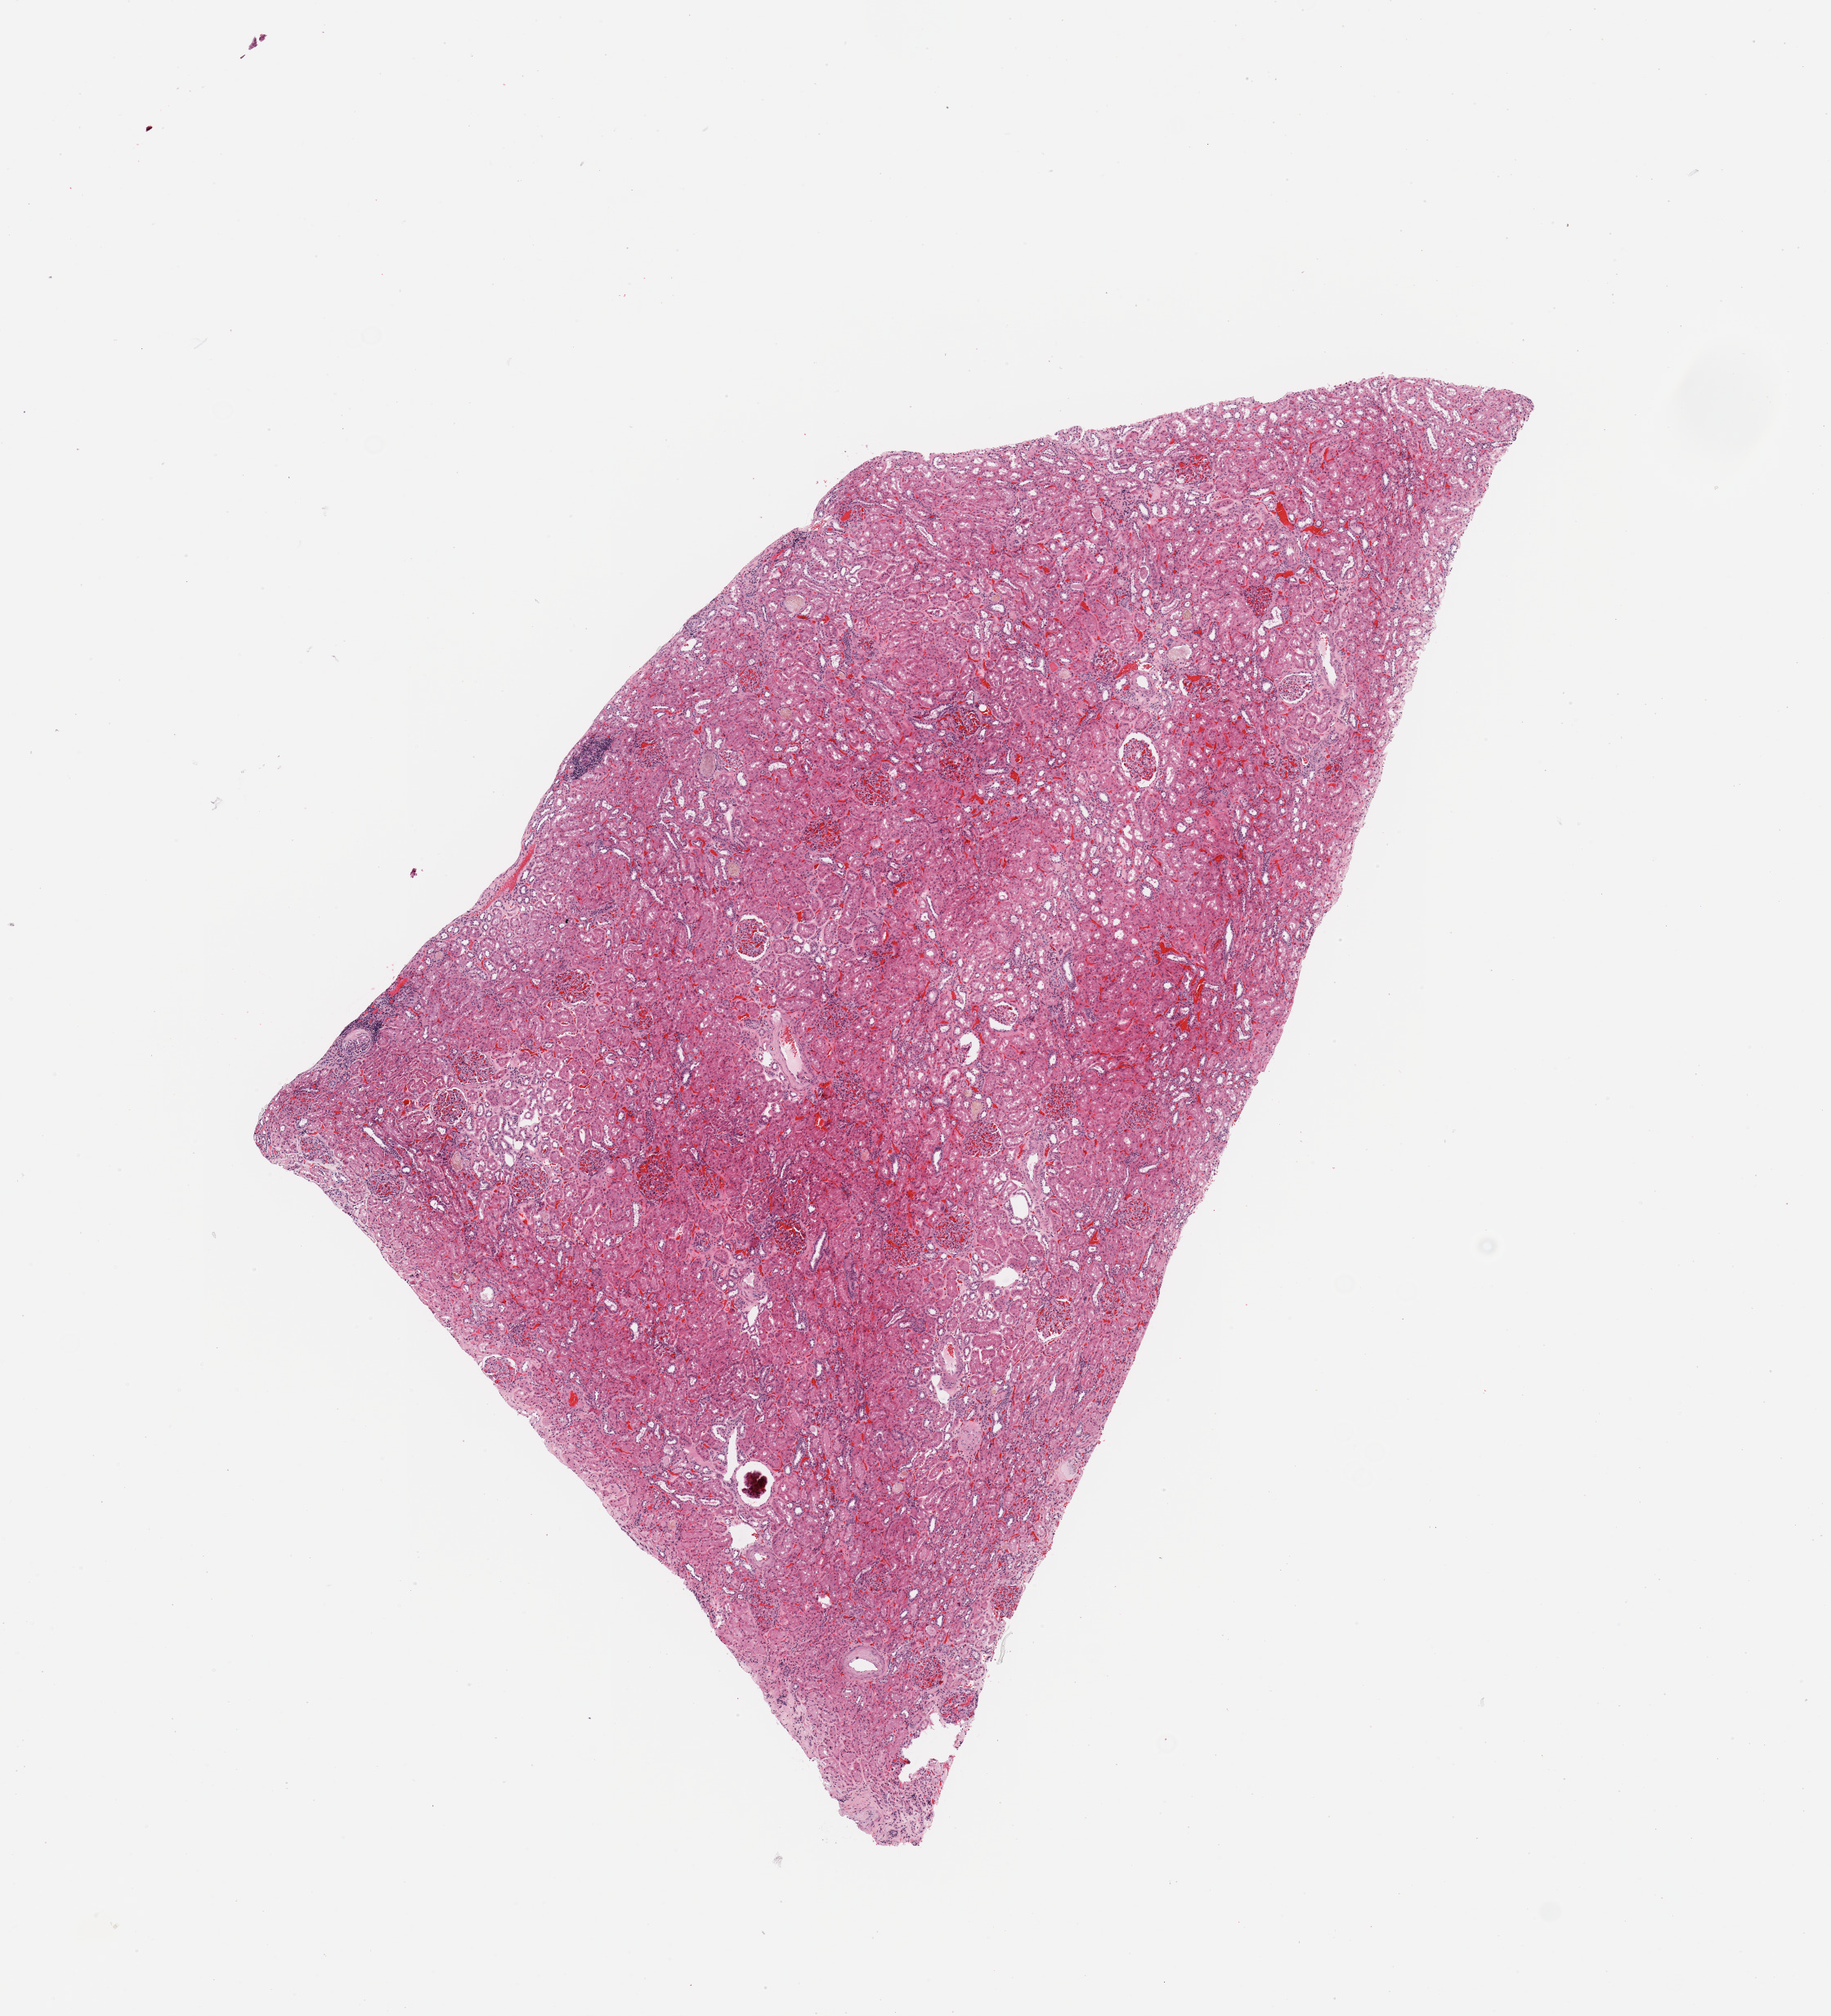
Digitized Hematoxylin and eosin (H&E) stained tissue section (whole slide) — a low-resolution overview of the entire scanned area, about 8.9 x 9.8 mm (from a 20x scan), normal (non-tumour) tissue sample, sampled site: kidney. Patient: male, age 59 years.
This section: normal (non-tumour) tissue from the same patient. Patient diagnosis: Renal cell carcinoma, NOS.